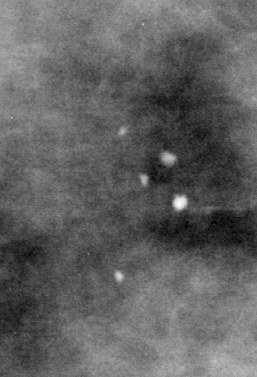
Cropped region of a digitized screen-film mammogram centred on a radiologist-marked abnormality; left breast; CC view.
Marked abnormality: calcifications, morphology pleomorphic, distribution clustered; BI-RADS assessment category 4; subtlety rating 5 on a 1 (subtle) to 5 (obvious) scale; pathology result (as recorded, not read from the image): benign.